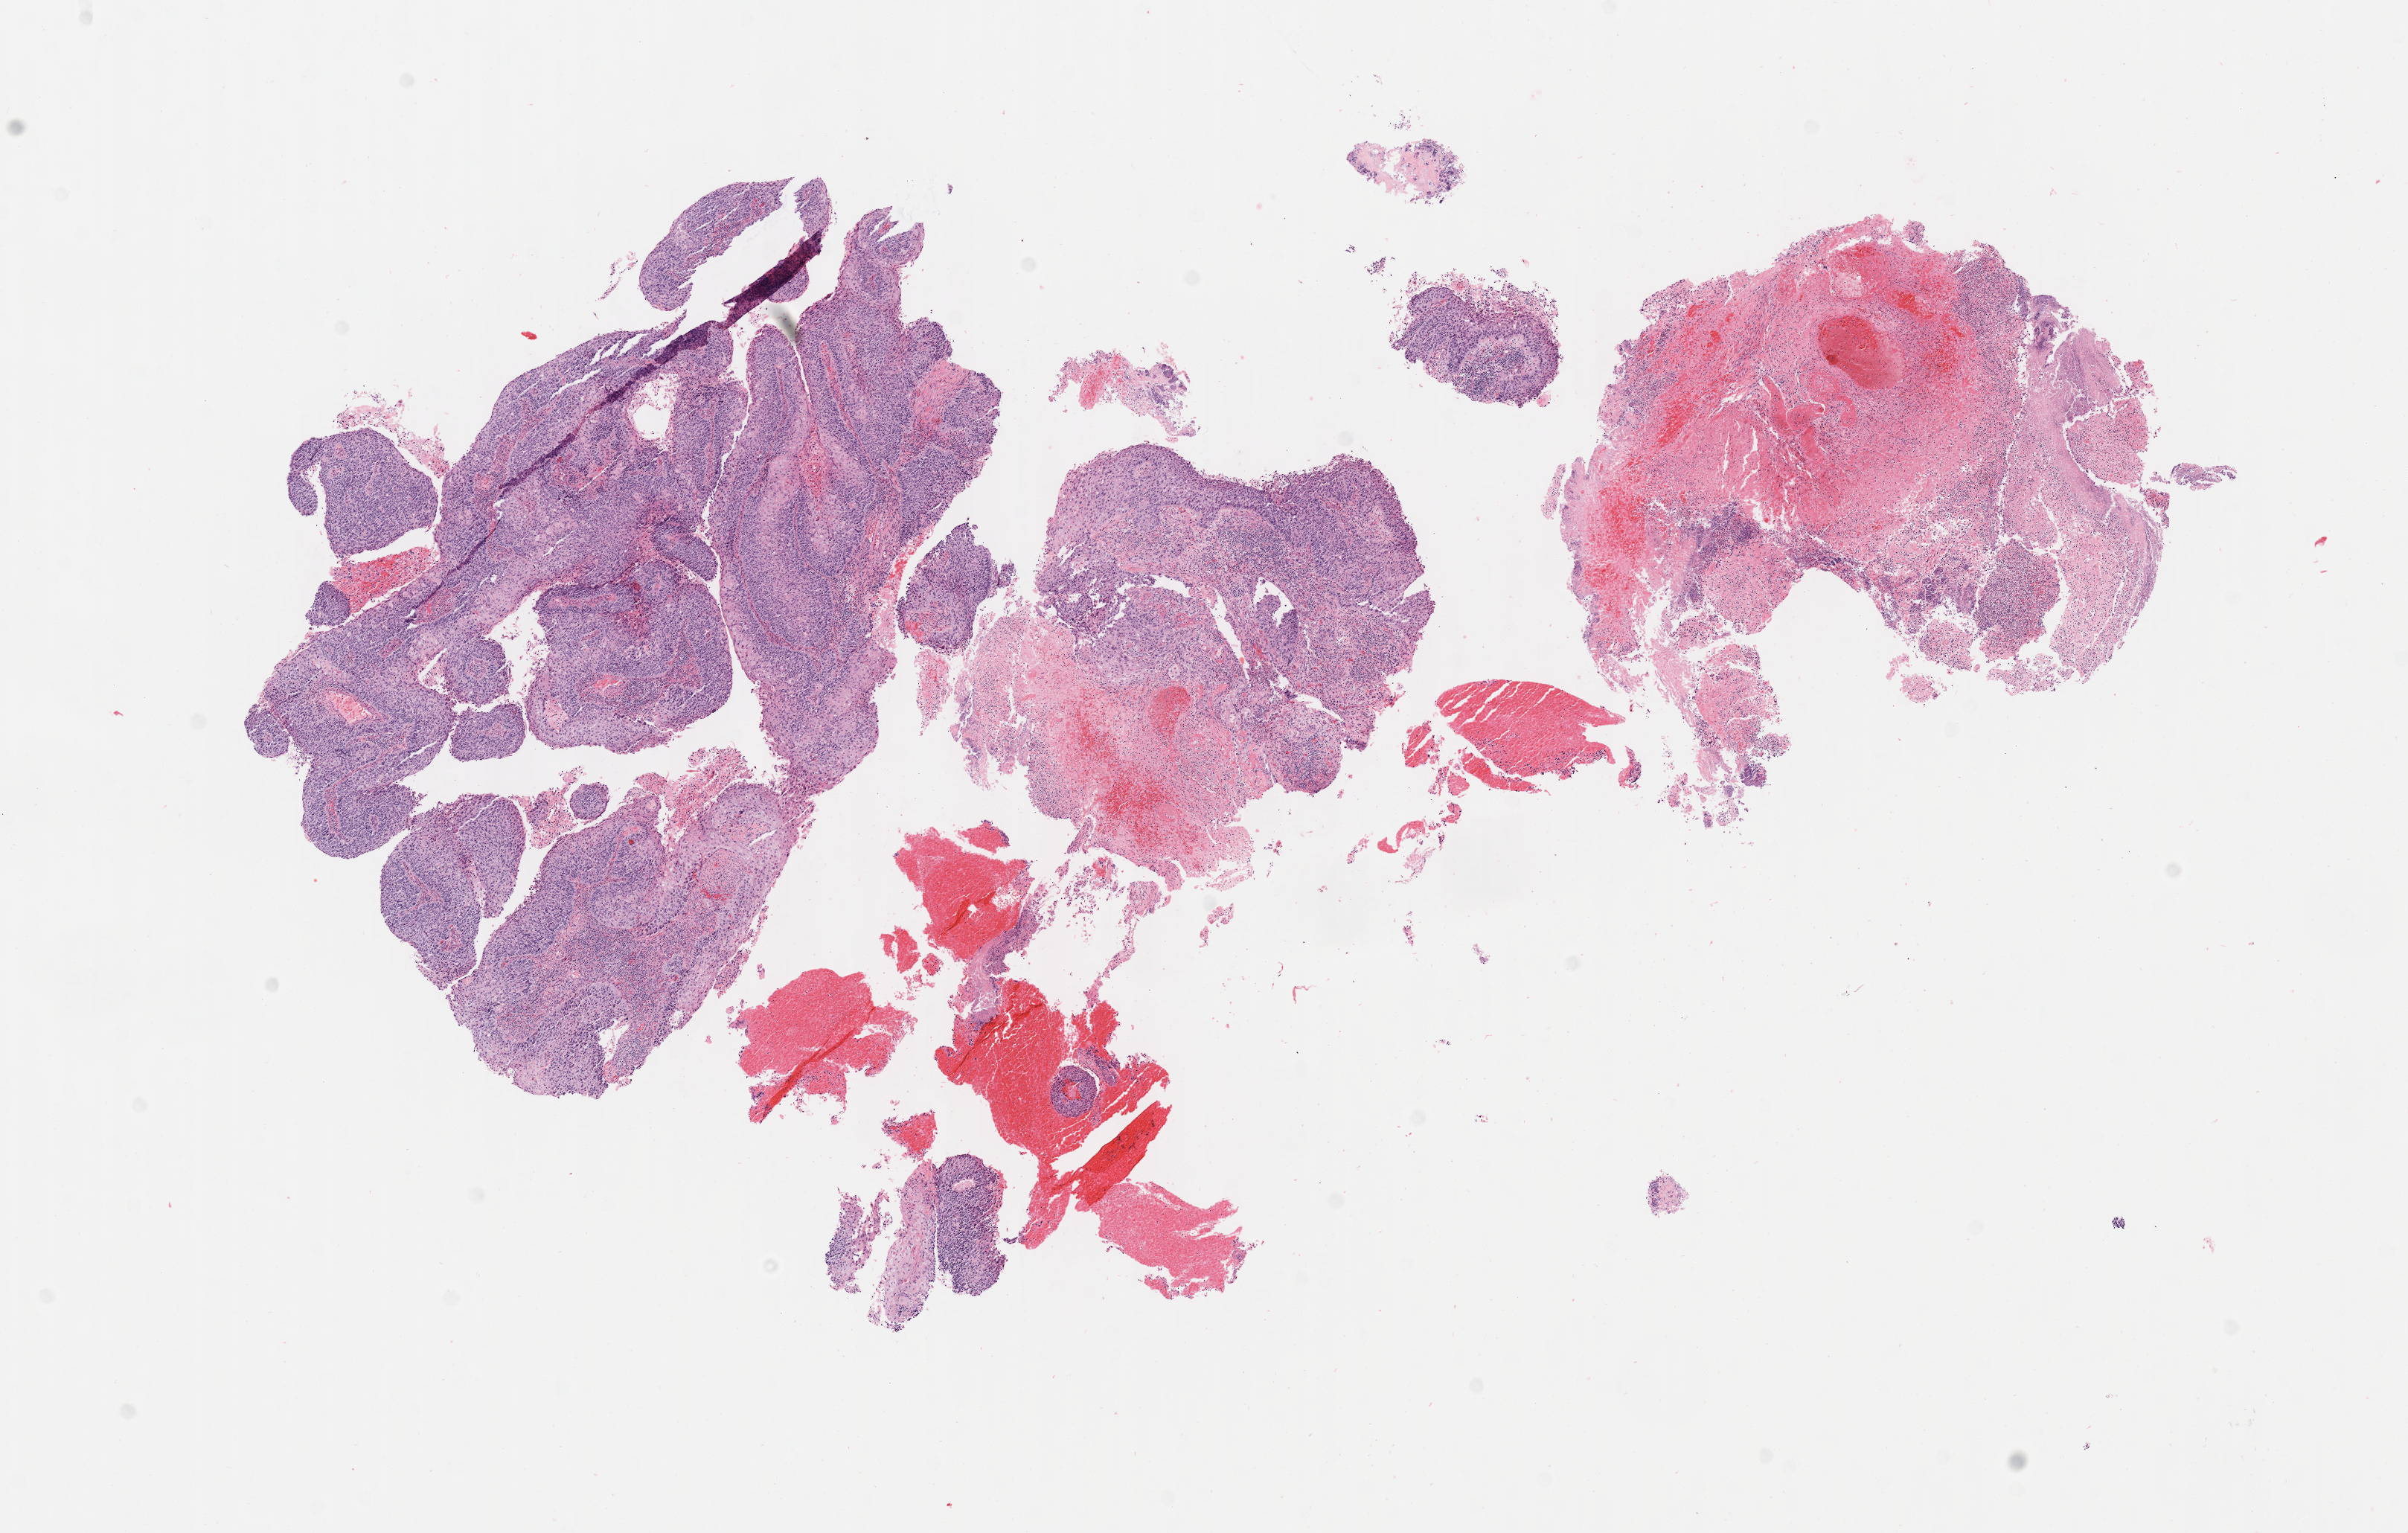
Digitized H&E-stained section — whole scanned area (about 13.1 x 8.3 mm) shown as a low-resolution overview. Tumor tissue. Site: cervix. Patient female; aged 46.
Histologic diagnosis: Squamous cell carcinoma, large cell, nonkeratinizing, NOS.